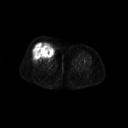
FDG PET of an extremity soft-tissue mass (from a PET/CT study), one axial slice. Slice 36 of 267 in the series (ordered by position). 3.27 mm slice thickness. 128 × 128 image matrix. Patient: female, 56 years. Case-level facts recorded for this patient, not image findings: histological type: malignant solitary fibrous tumor; grade: intermediate; site of the primary tumour: right thigh.
Structures marked on this image (expert contour drawn on MRI and transferred to this co-registered scan by the dataset authors):
- gross tumour volume including surrounding oedema: bounding box <33,42,56,59> (left, top, right, bottom; pixels)
- gross tumour volume (mass): <34,42,55,59>